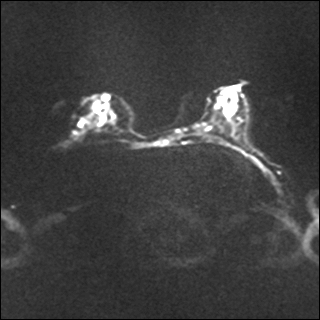
Breast MRI, one axial slice; position 16 of 35 along the scan axis; diffusion-weighted series; image 2 of 4 stored at this slice position (different b-values; order by instance number); 1.5 T; 4 mm slice thickness; 320 × 320 image matrix, field of view 317 × 317 mm. Female patient.
Annotated regions visible in this slice (expert manual segmentation):
- tumour on diffusion-weighted imaging: bounding box (x1, y1, x2, y2) in pixels: (78, 95, 109, 128)